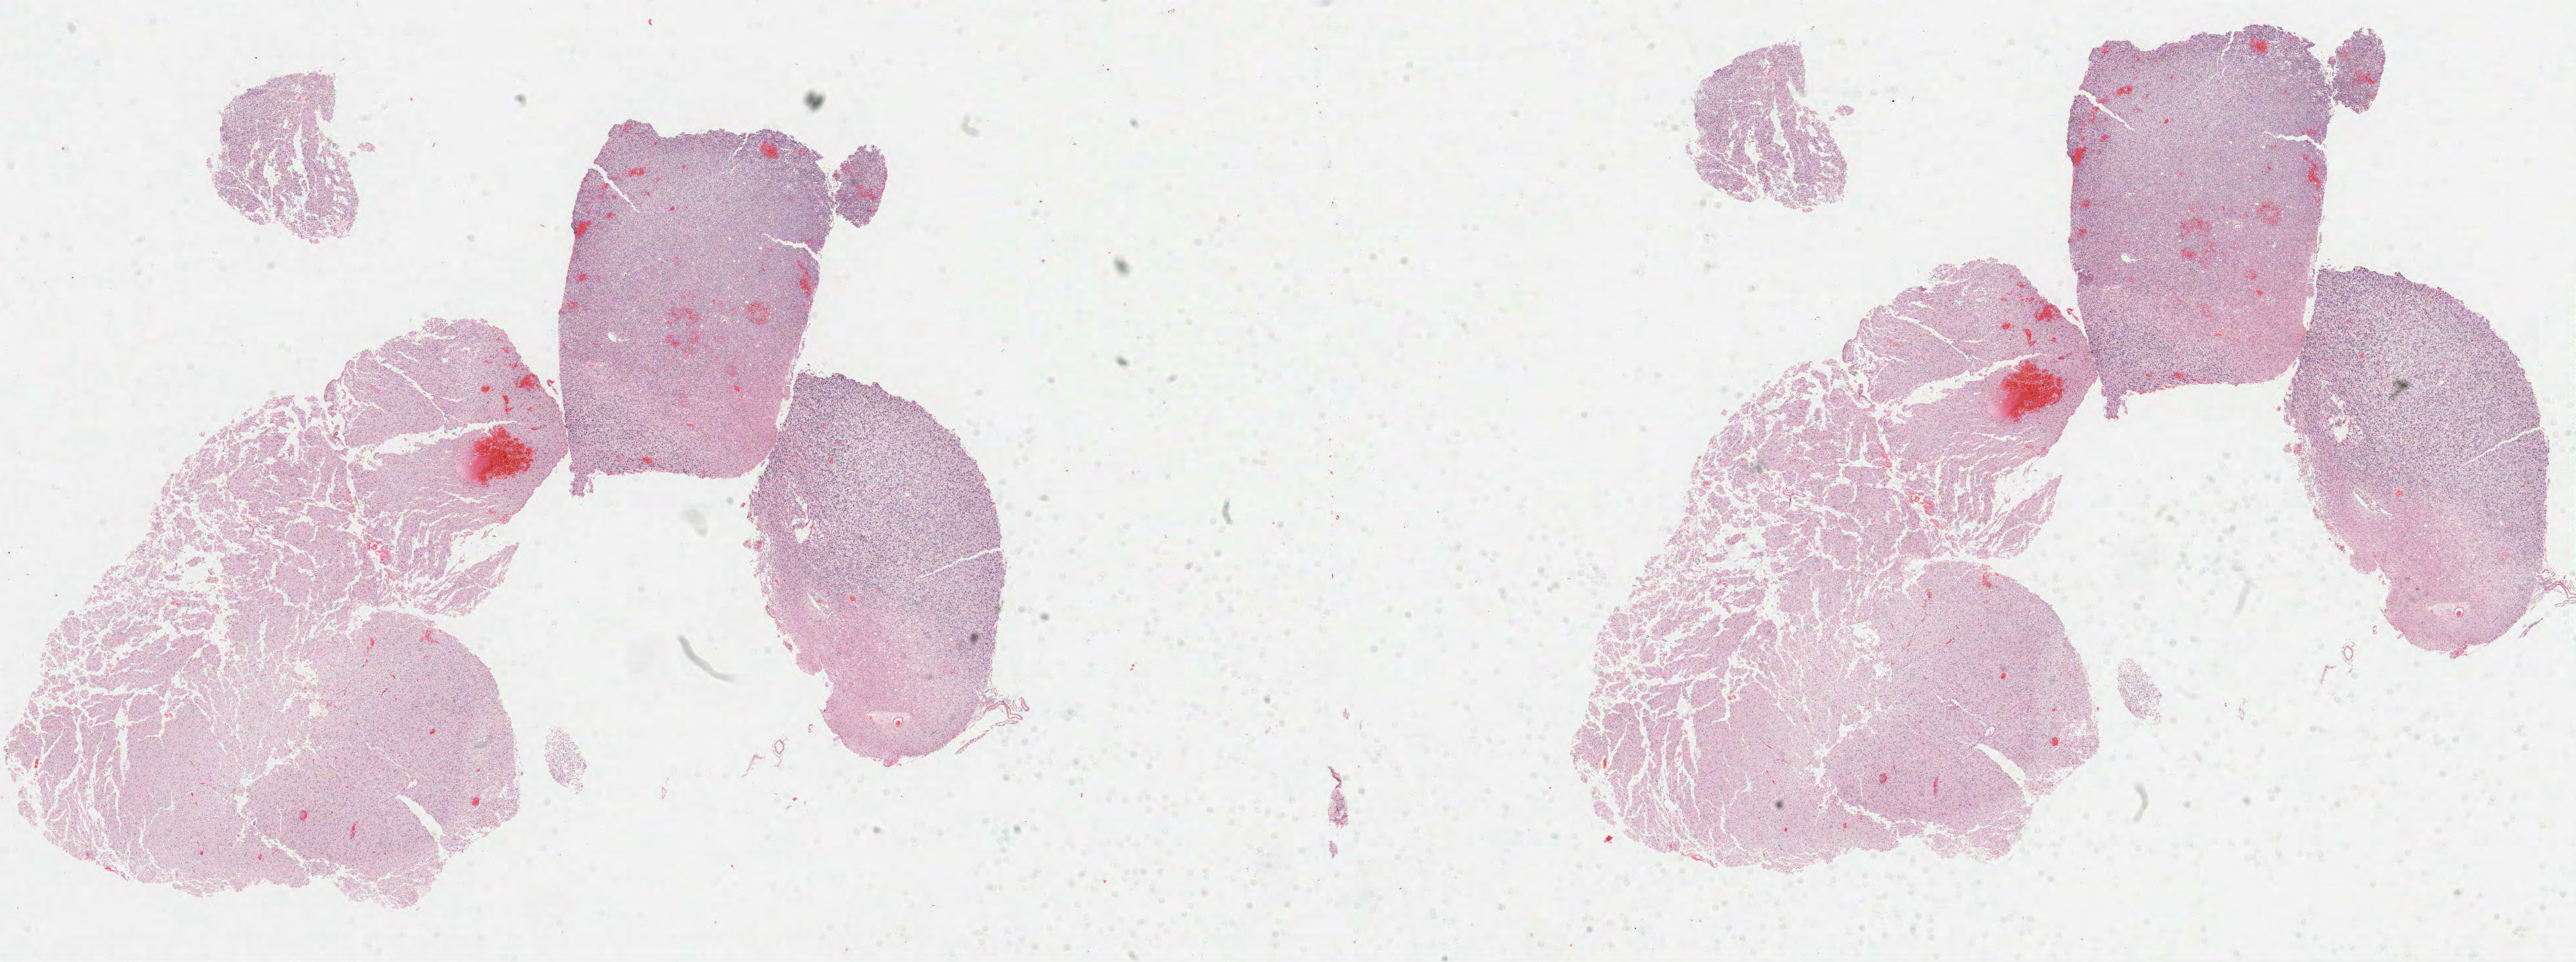
Digitized H&E-stained tissue section (whole slide), shown as a low-resolution overview of the whole scanned area (about 31.4 x 11.7 mm, slide scanned at 40x). Formalin-fixed paraffin-embedded (FFPE) diagnostic section. Sample: primary tumour, brain. Male patient; age at initial diagnosis 62 years. Histologic grade: G2 (moderately differentiated).
Laterality: left. Pathologic diagnosis: Oligodendroglioma, NOS (cerebrum).